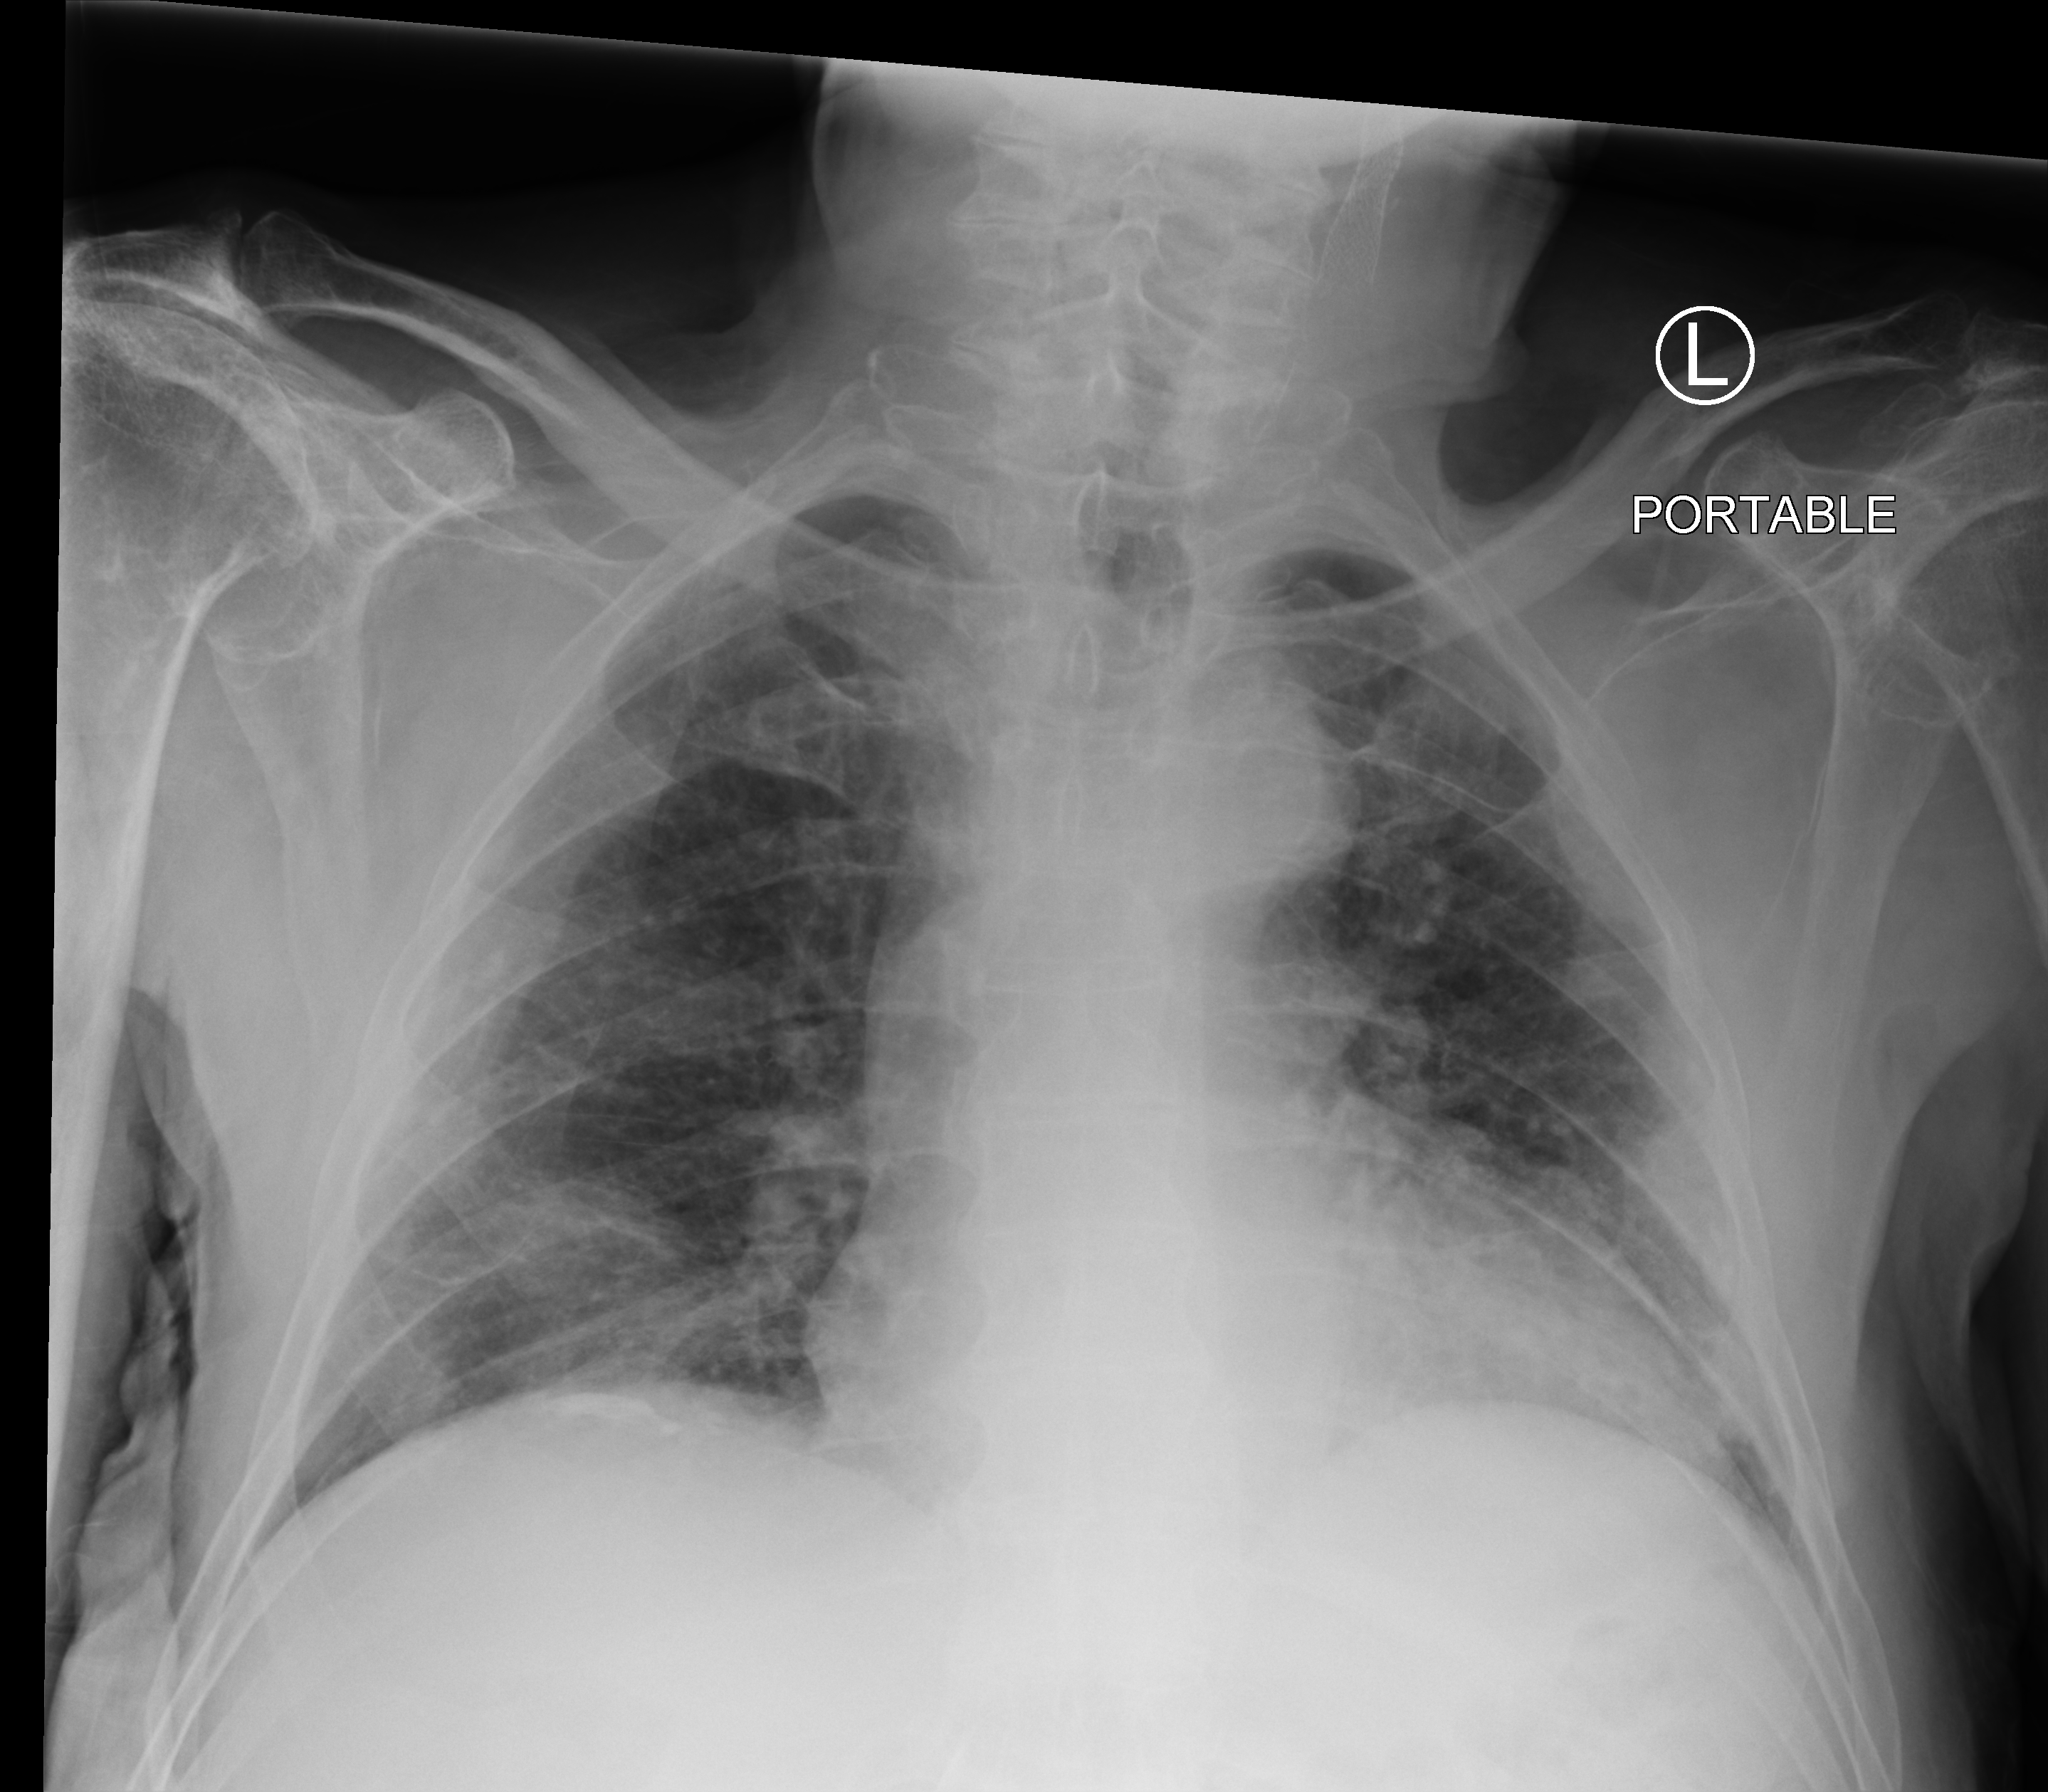
Bedside chest radiograph (computed radiography); anteroposterior (AP) projection. Male patient hospitalised with COVID-19, age 75–90 years.
From the hospital-stay record, not from the radiograph (when in the stay this image was taken is not recorded):
- length of hospital stay: 1 day
- mechanically ventilated during this hospital stay: no